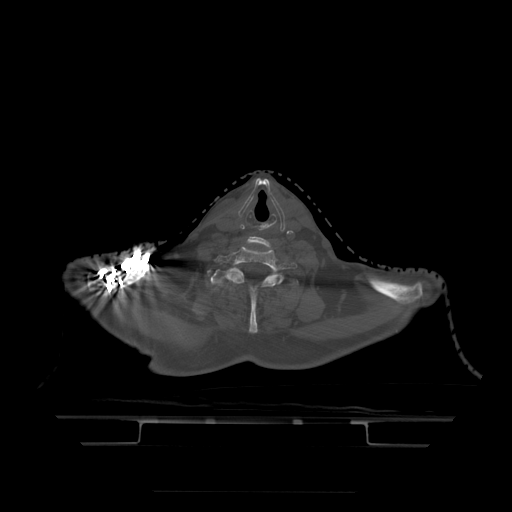
CT including the spine, one axial slice. Position 407 of 522 along the scan axis. Bone window (W 1800 / L 400 HU). 1.25 mm slice thickness. 512 × 512 image matrix, field of view 436 × 436 mm. Patient age 68 years. Case-level facts recorded for this patient, not image findings: primary cancer: urothelial.
Structures marked on this image (semi-automatic segmentation, software-assisted and operator-edited):
- T1 vertebra: bounding box [x1, y1, x2, y2] px = [211, 268, 300, 334]